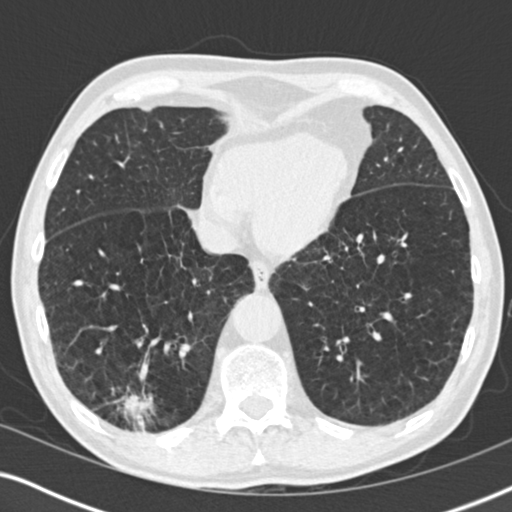
Low-dose screening chest CT, one axial slice; slice 62 of 196 in the series (ordered by position); 120 kVp; lung window (W 1500 / L -600 HU); 2 mm slice thickness; 512 × 512 image matrix, field of view 330 × 330 mm.
Outlined on this slice (expert manual segmentation):
- lesion 3 (tumor, lower lobe of right lung): bounding box <122,395,154,428> (left, top, right, bottom; pixels)